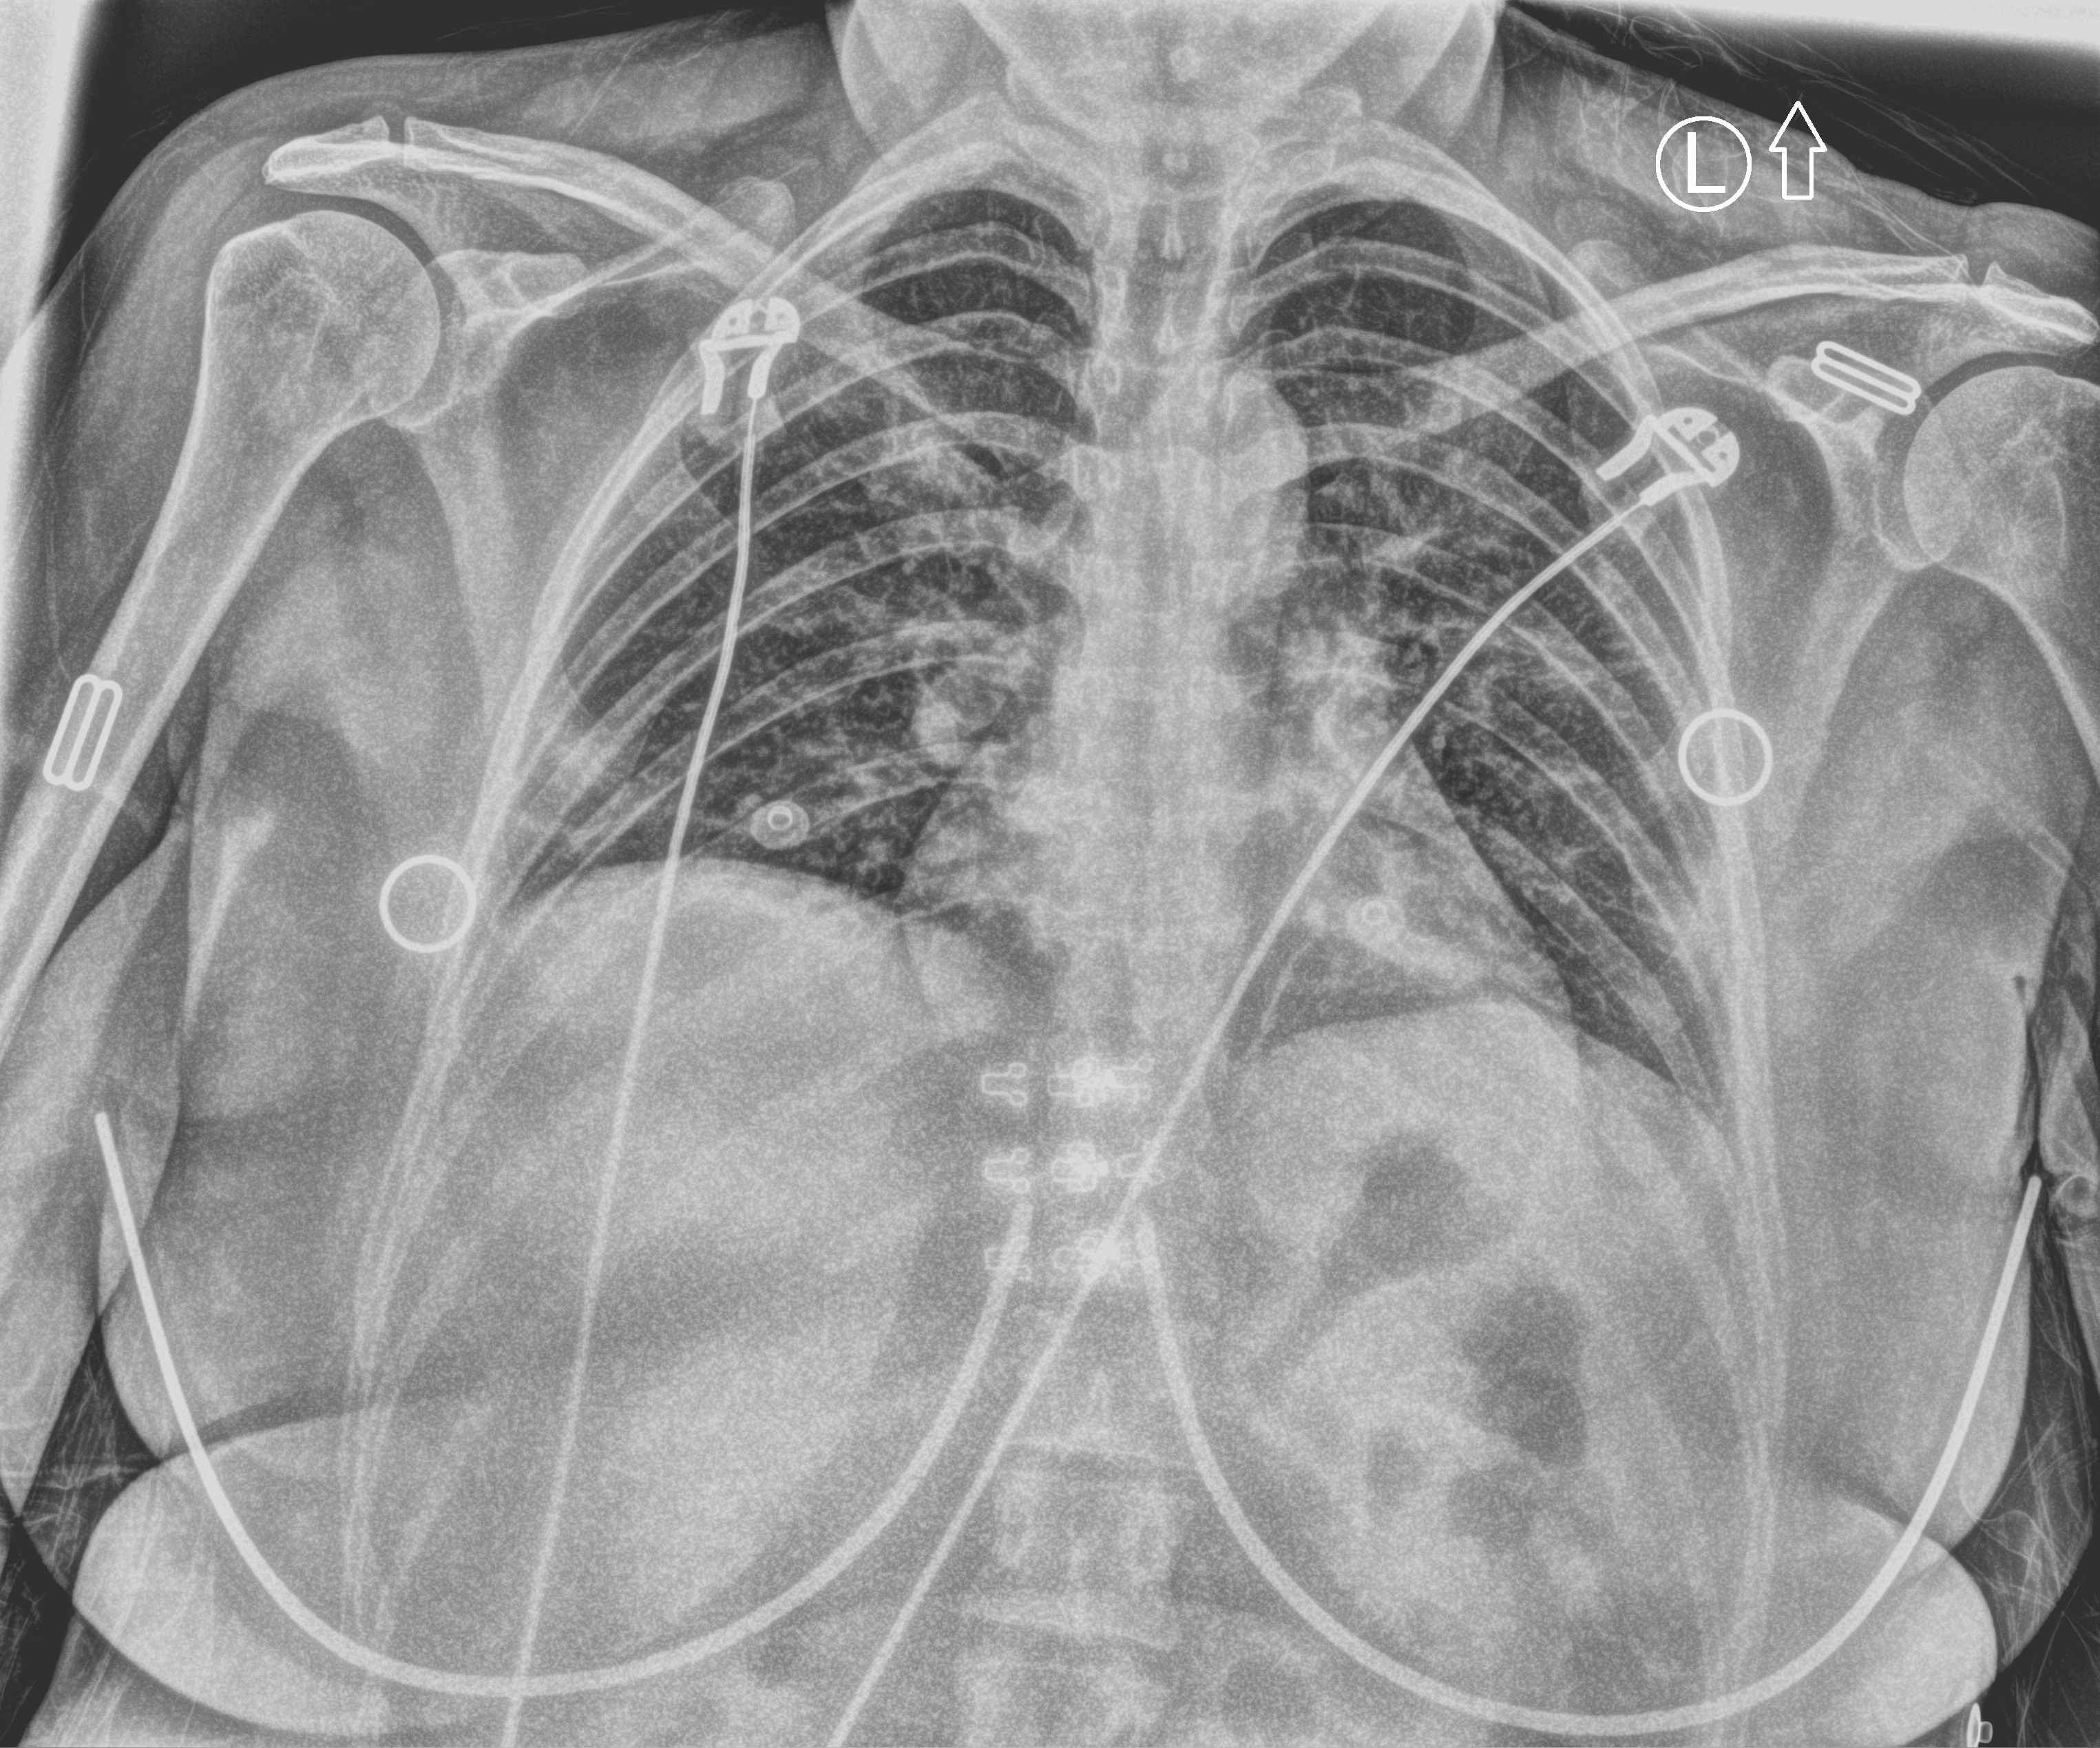
Chest X-ray (portable); anteroposterior (AP) projection. Patient hospitalised with COVID-19; female, aged 18–59 years.
Admission-level facts for this patient (not findings on this image; timing relative to this image not recorded):
- admitted to intensive care during this hospital stay: no